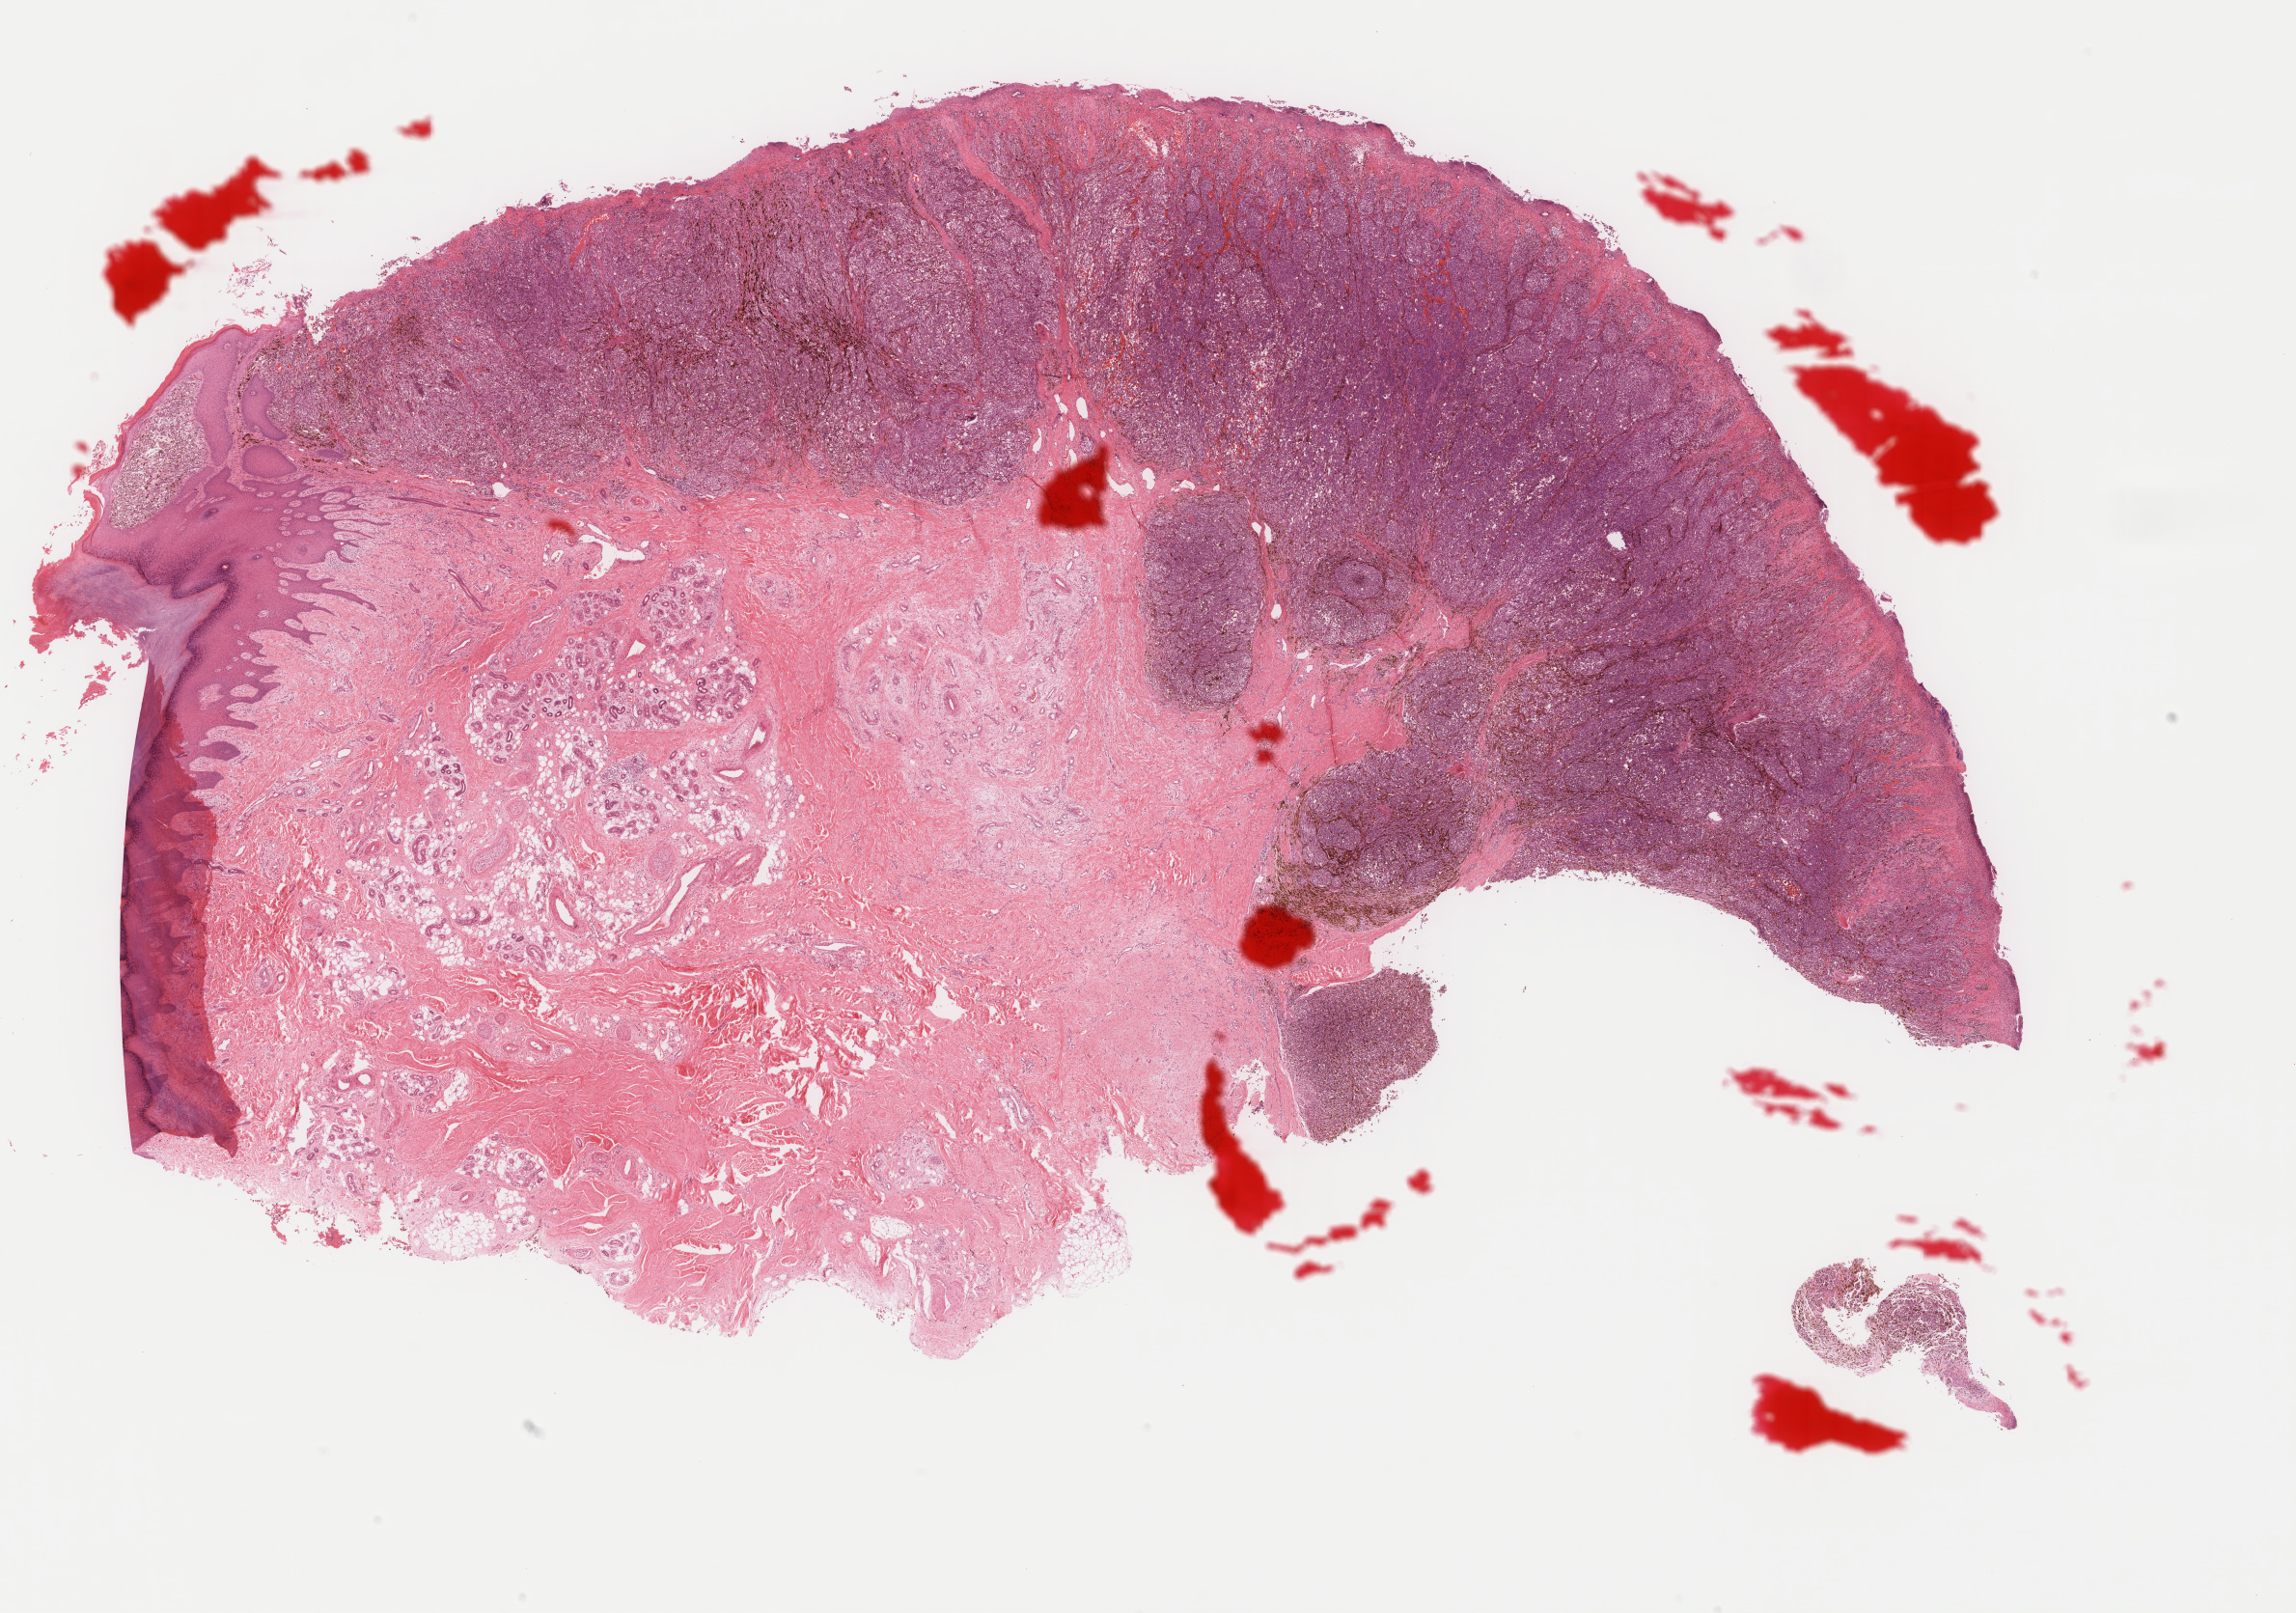
Hematoxylin and eosin (H&E) stained whole-slide image, shown as a low-resolution overview of the whole scanned area (about 18.9 x 13.3 mm, slide scanned at 40x). Formalin-fixed paraffin-embedded (FFPE) diagnostic section. Sample: primary tumour, skin. Female, age 65 years at initial diagnosis.
- diagnosis: Malignant melanoma, NOS